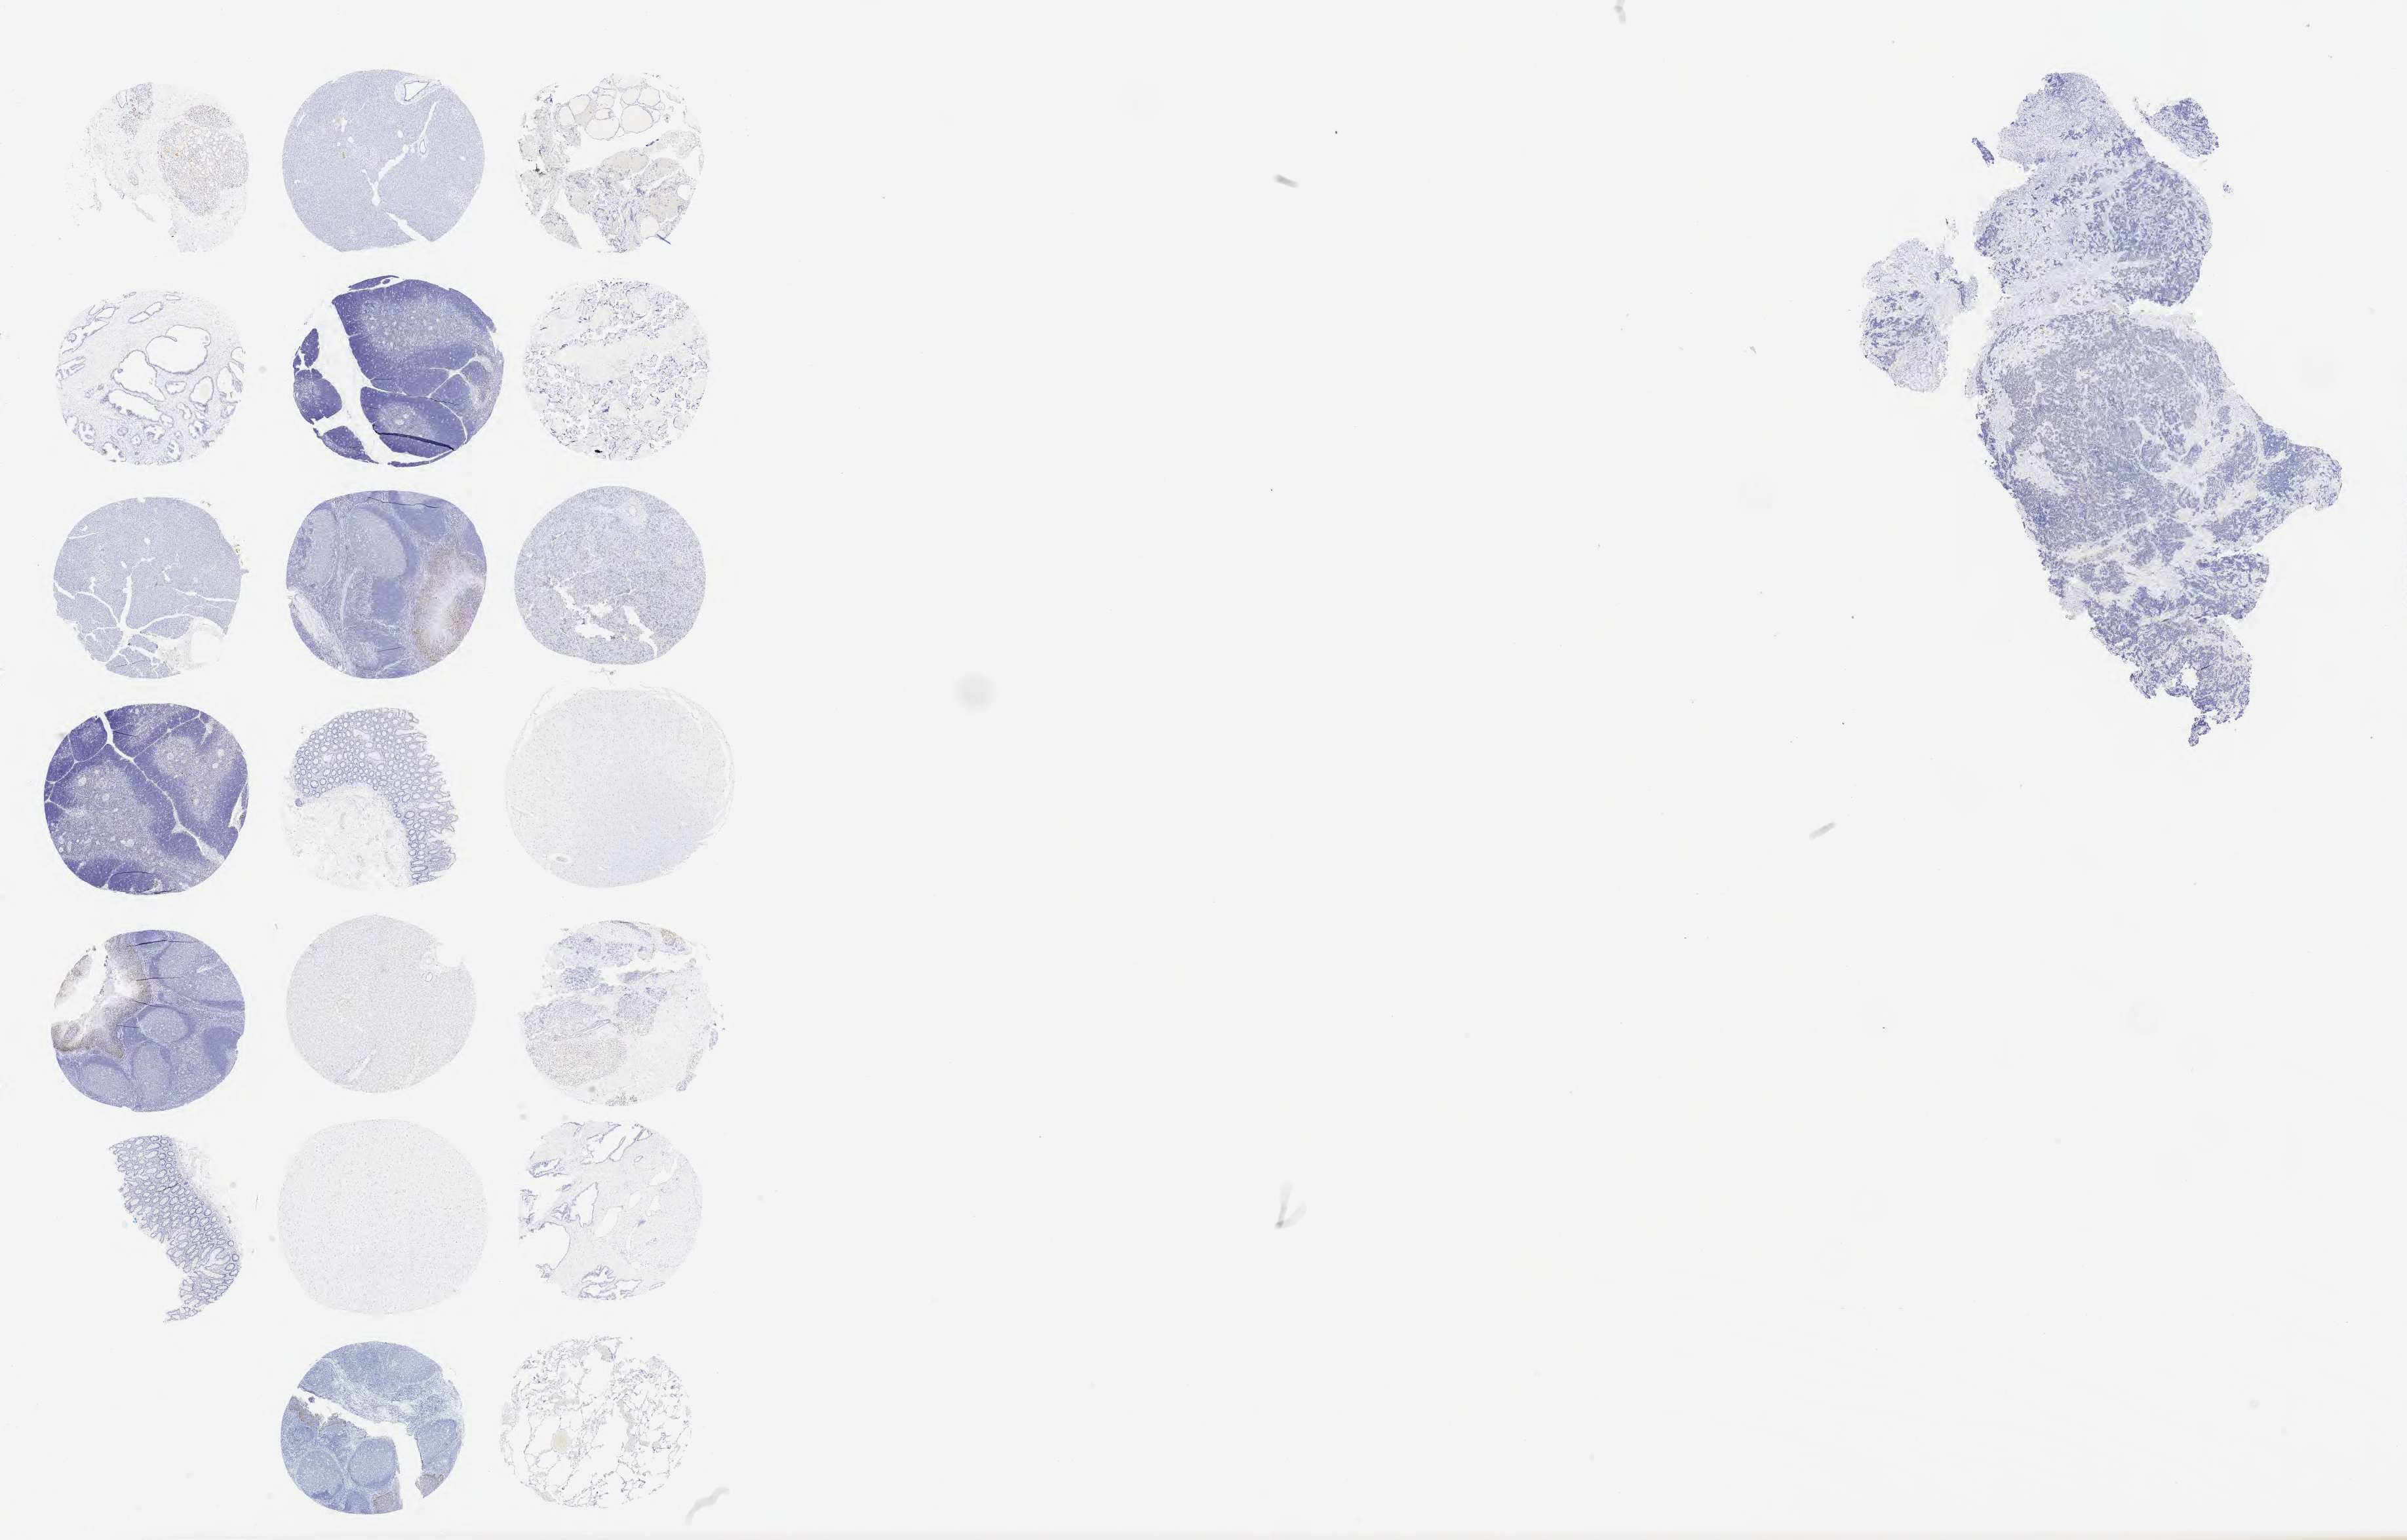
Whole-slide image, immunohistochemical stain for p63 — shown as a low-resolution overview of the whole scanned area (about 29.7 x 19.0 mm), tumor tissue, anatomic site: cervix. Patient female; 43 years old.
Diagnosis: Lymphoepithelial carcinoma.